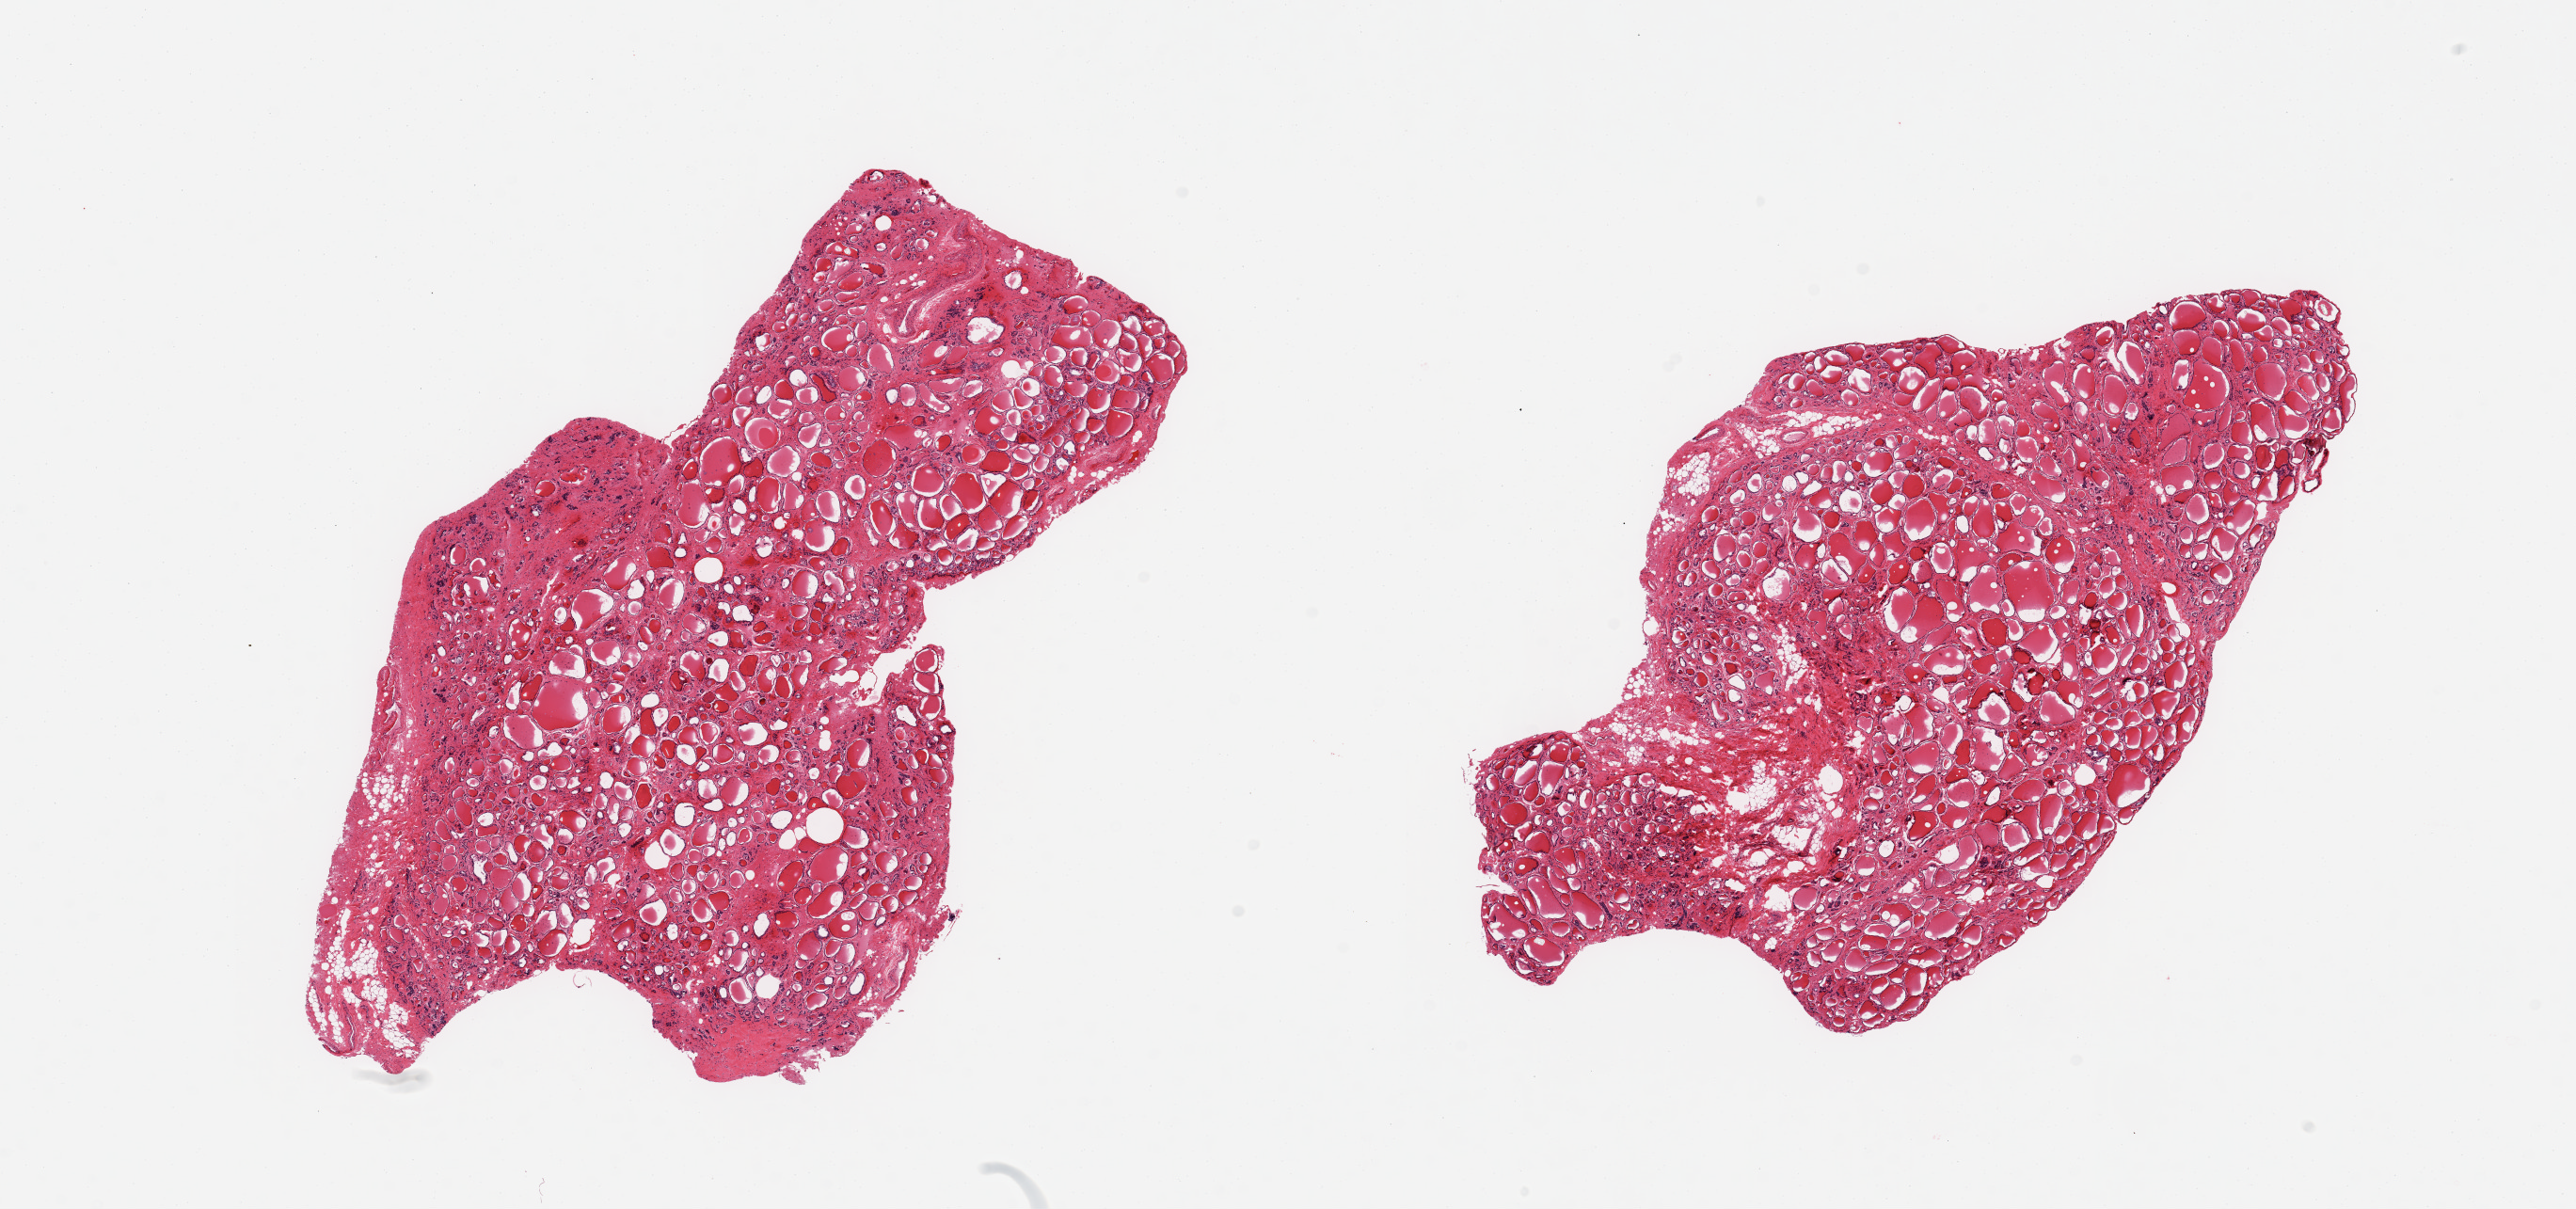
Digitized H&E-stained section — shown as a low-resolution overview of the whole scanned area (about 21.7 x 10.2 mm, slide scanned at 20x), PAXgene-fixed paraffin-embedded (PFPE) section, sampled site (target tissue): thyroid, donor tissue sample. Donor: male.
Reviewer comment on this tissue sample: 2 pieces; 10% & 5% fibrofatty content.